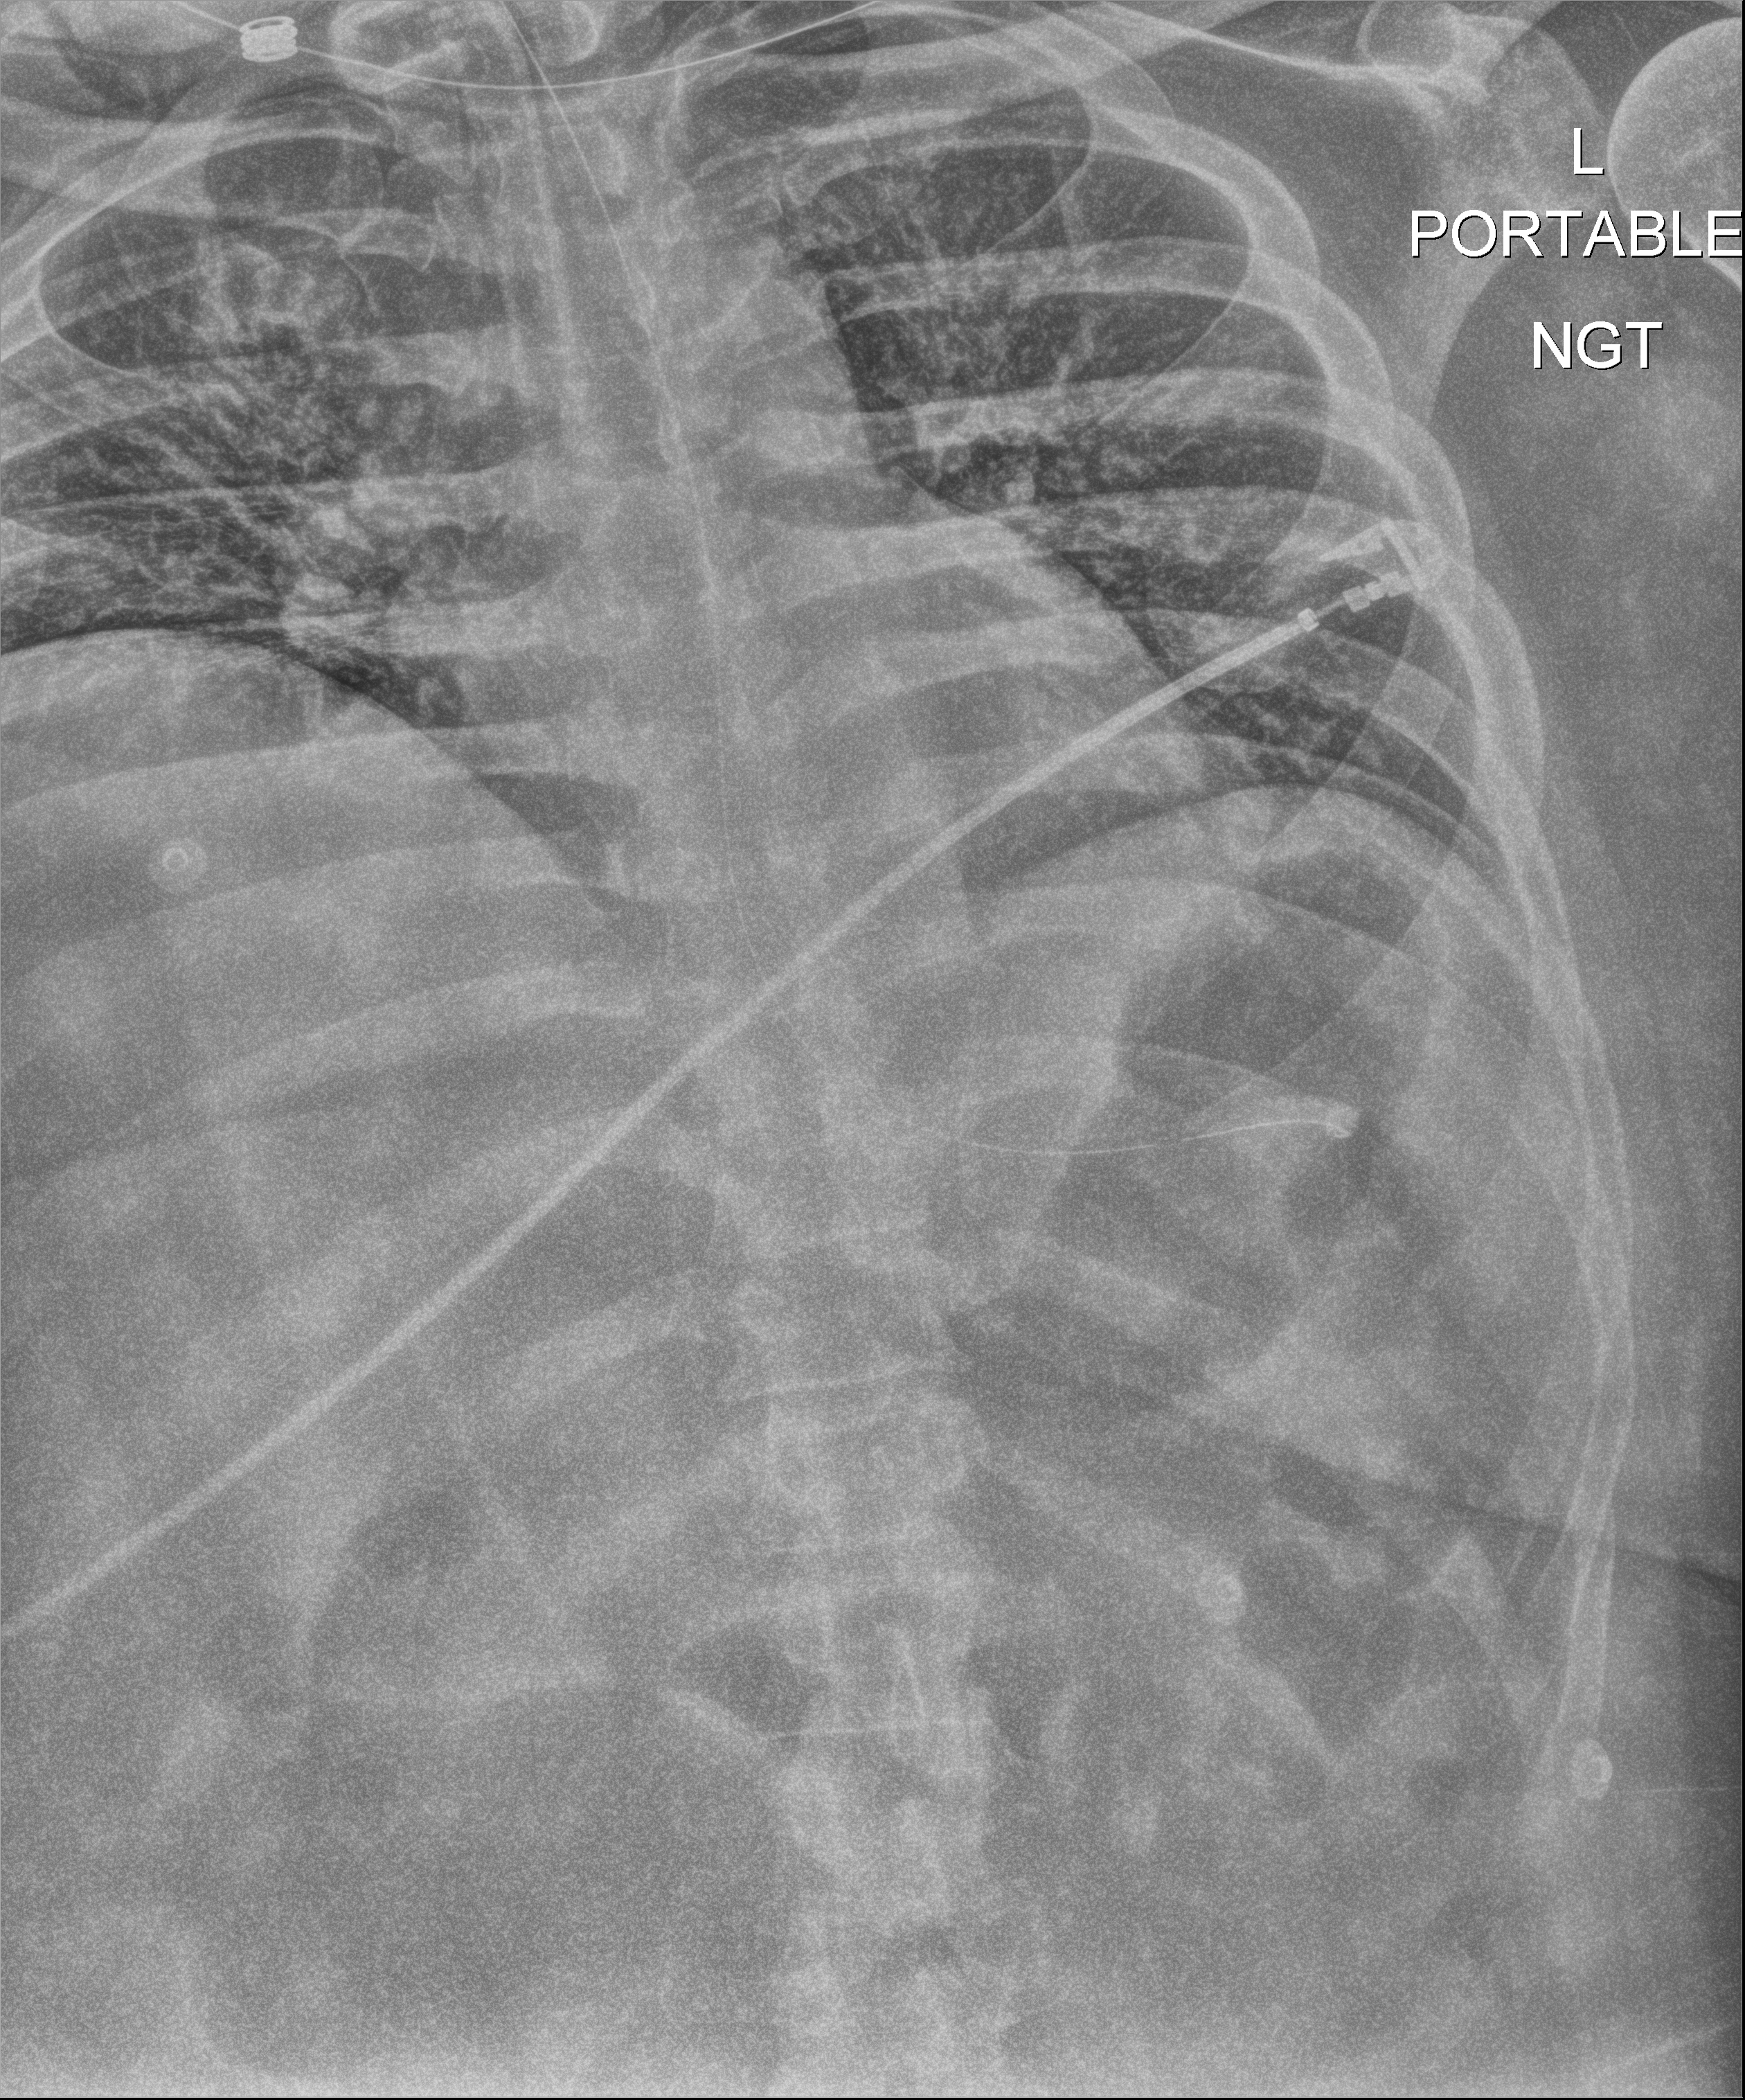
Chest X-ray (portable); anteroposterior (AP) projection. Male patient hospitalised with COVID-19, age 18–59 years.
From the hospital-stay record, not from the radiograph (when in the stay this image was taken is not recorded):
- mechanically ventilated during this hospital stay: yes
- hypertension (admission record): no
- admitted to intensive care during this hospital stay: yes